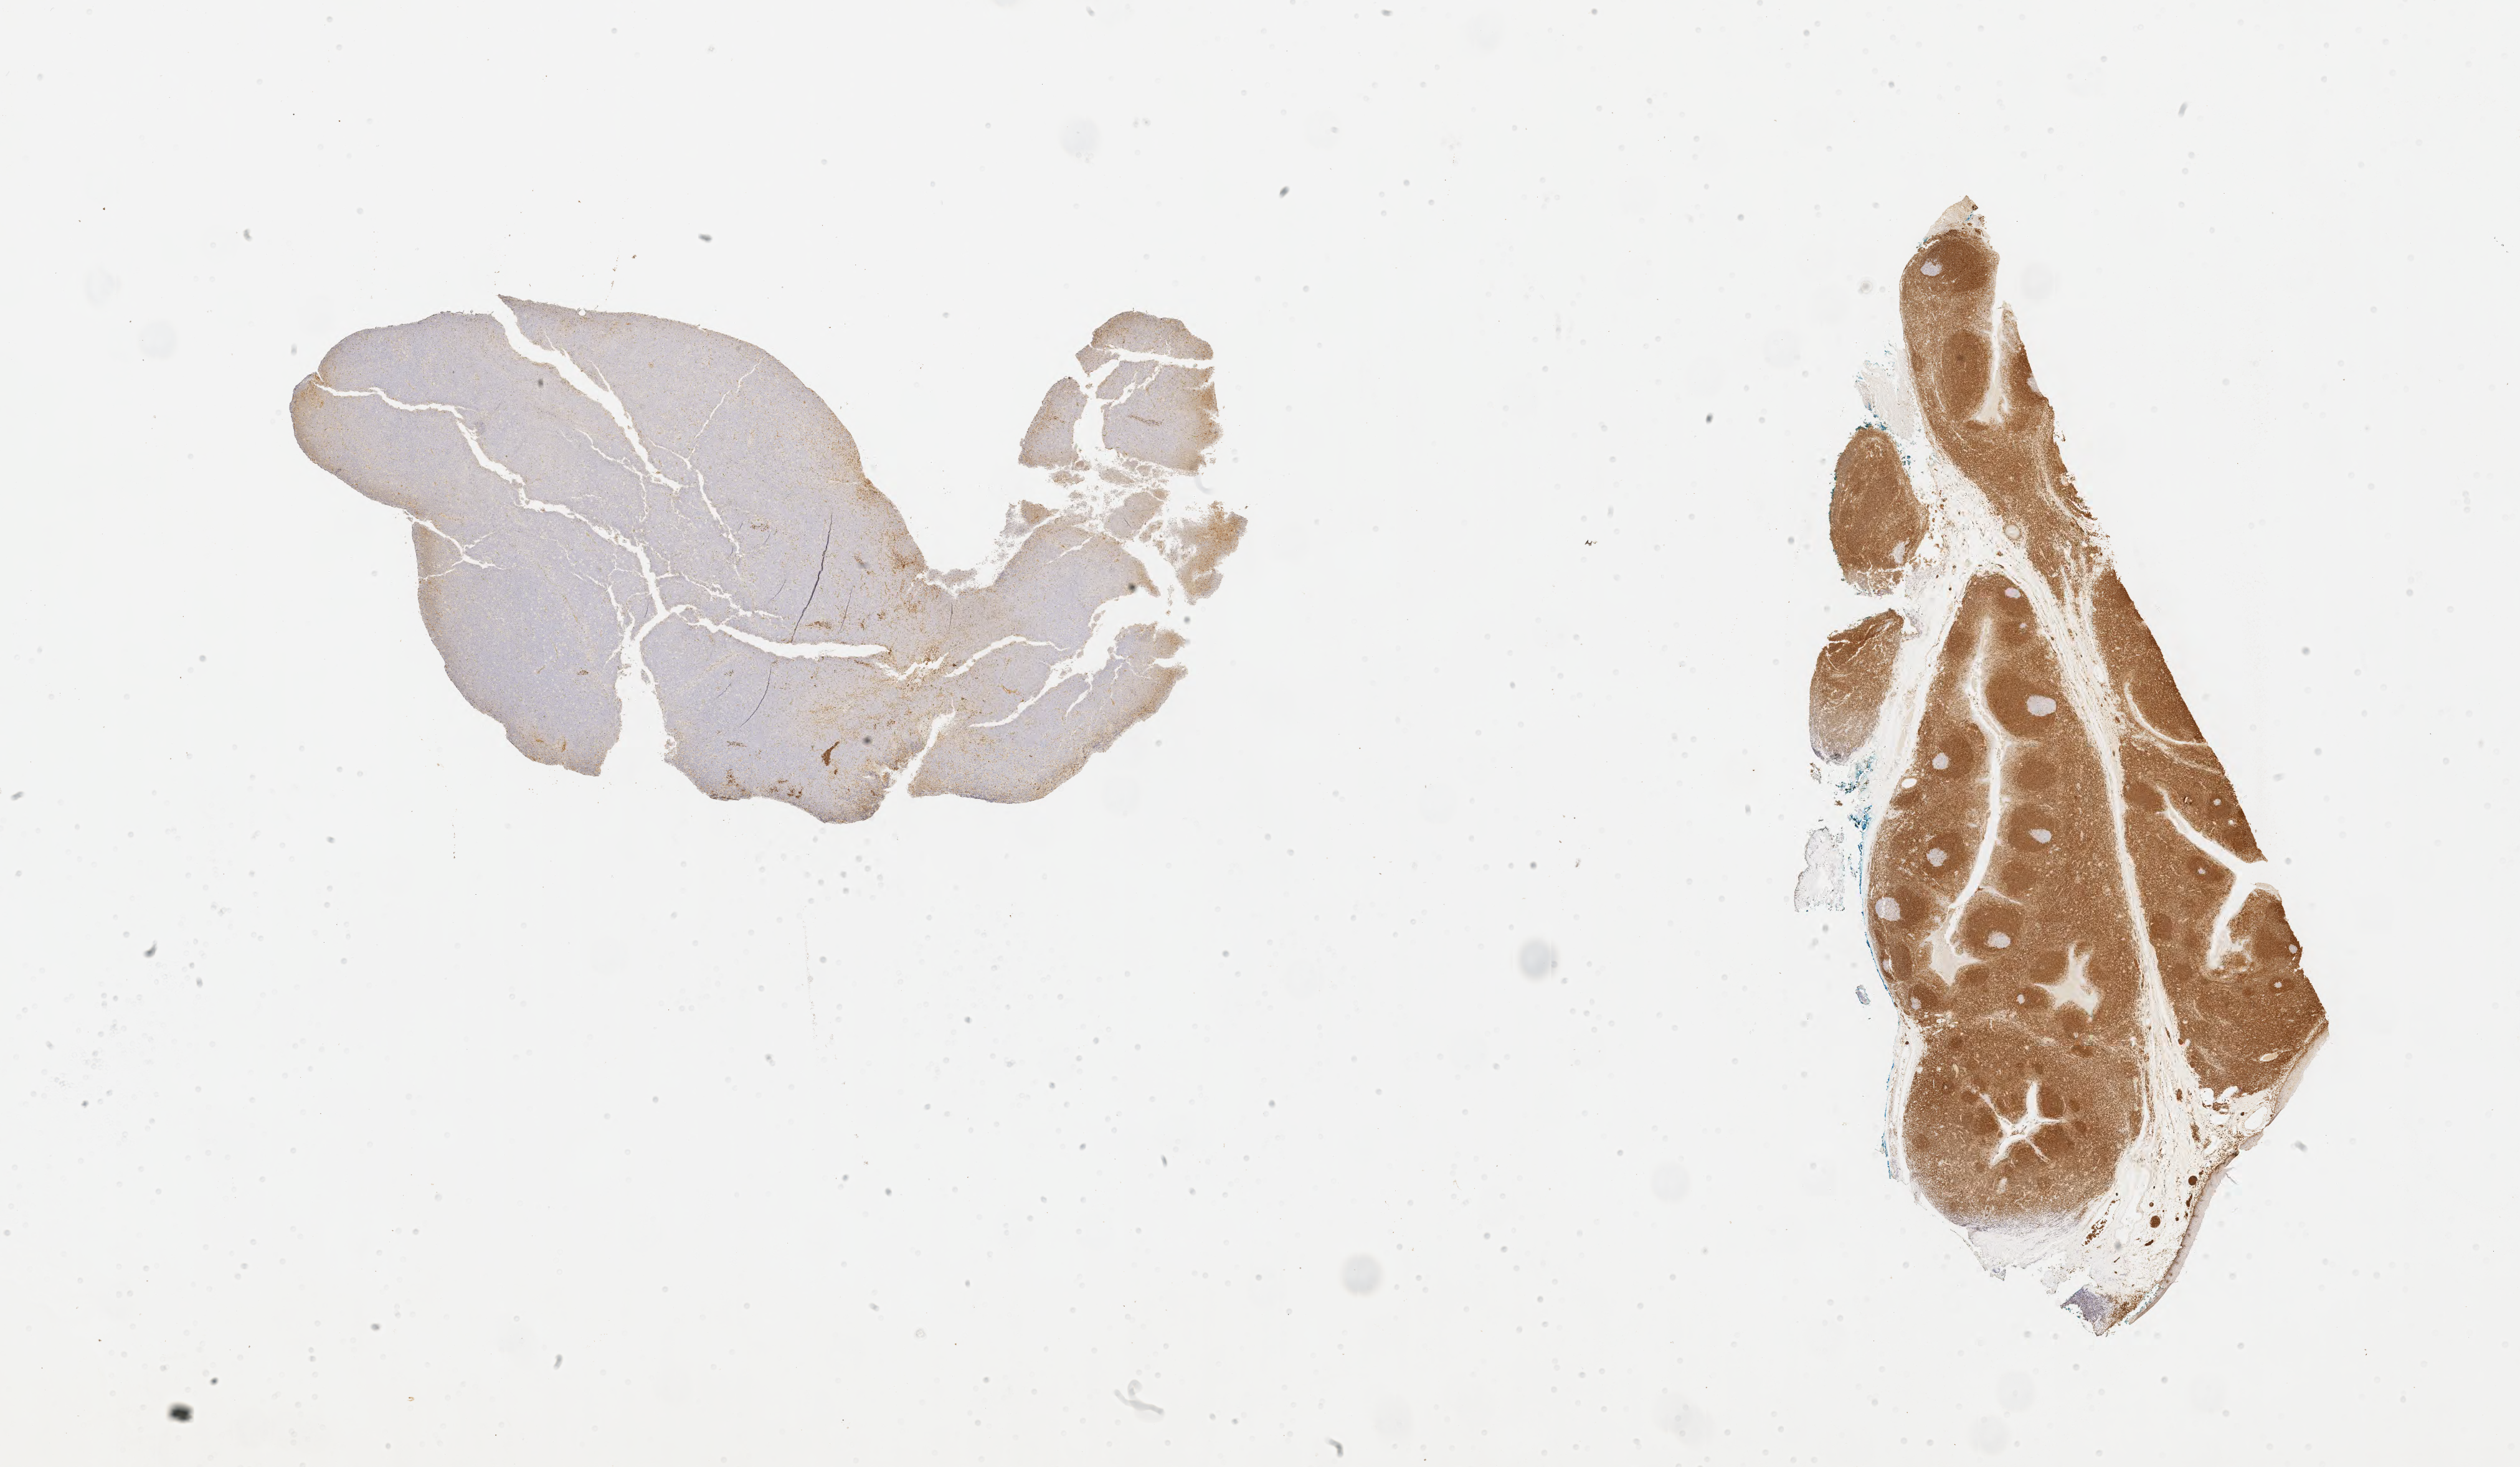
IHC for BCL2, whole-slide image, a low-resolution overview of the entire scanned area, about 32.7 x 19.0 mm. Specimen: tumor tissue. Anatomic site: lymph node of head and neck. Male patient; age at initial diagnosis 5 years.
Diagnosis: Burkitt lymphoma, NOS.